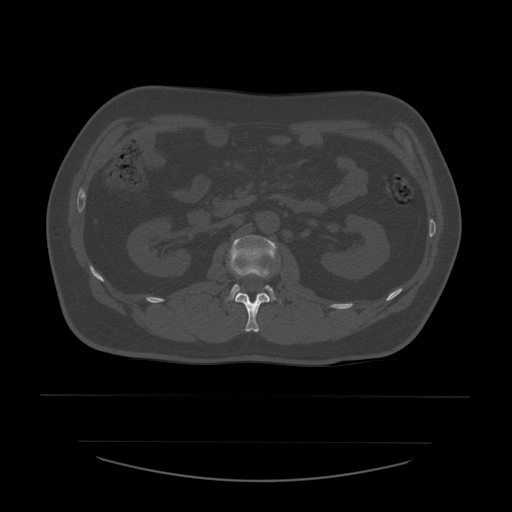
CT including the spine, one axial slice. Slice 214 of 532 in the series (ordered by position). 120 kVp. Bone window (W 1800 / L 400 HU). 512 × 512 image matrix, field of view 441 × 441 mm. Patient age 44 years. From the clinical record (not read from this slice): primary cancer: soft tissue sarcoma.
Structures marked on this image (semi-automatic segmentation, software-assisted and operator-edited):
- L1 vertebra: bounding box <235,293,270,332> (left, top, right, bottom; pixels)
- L2 vertebra: <229,235,277,301>